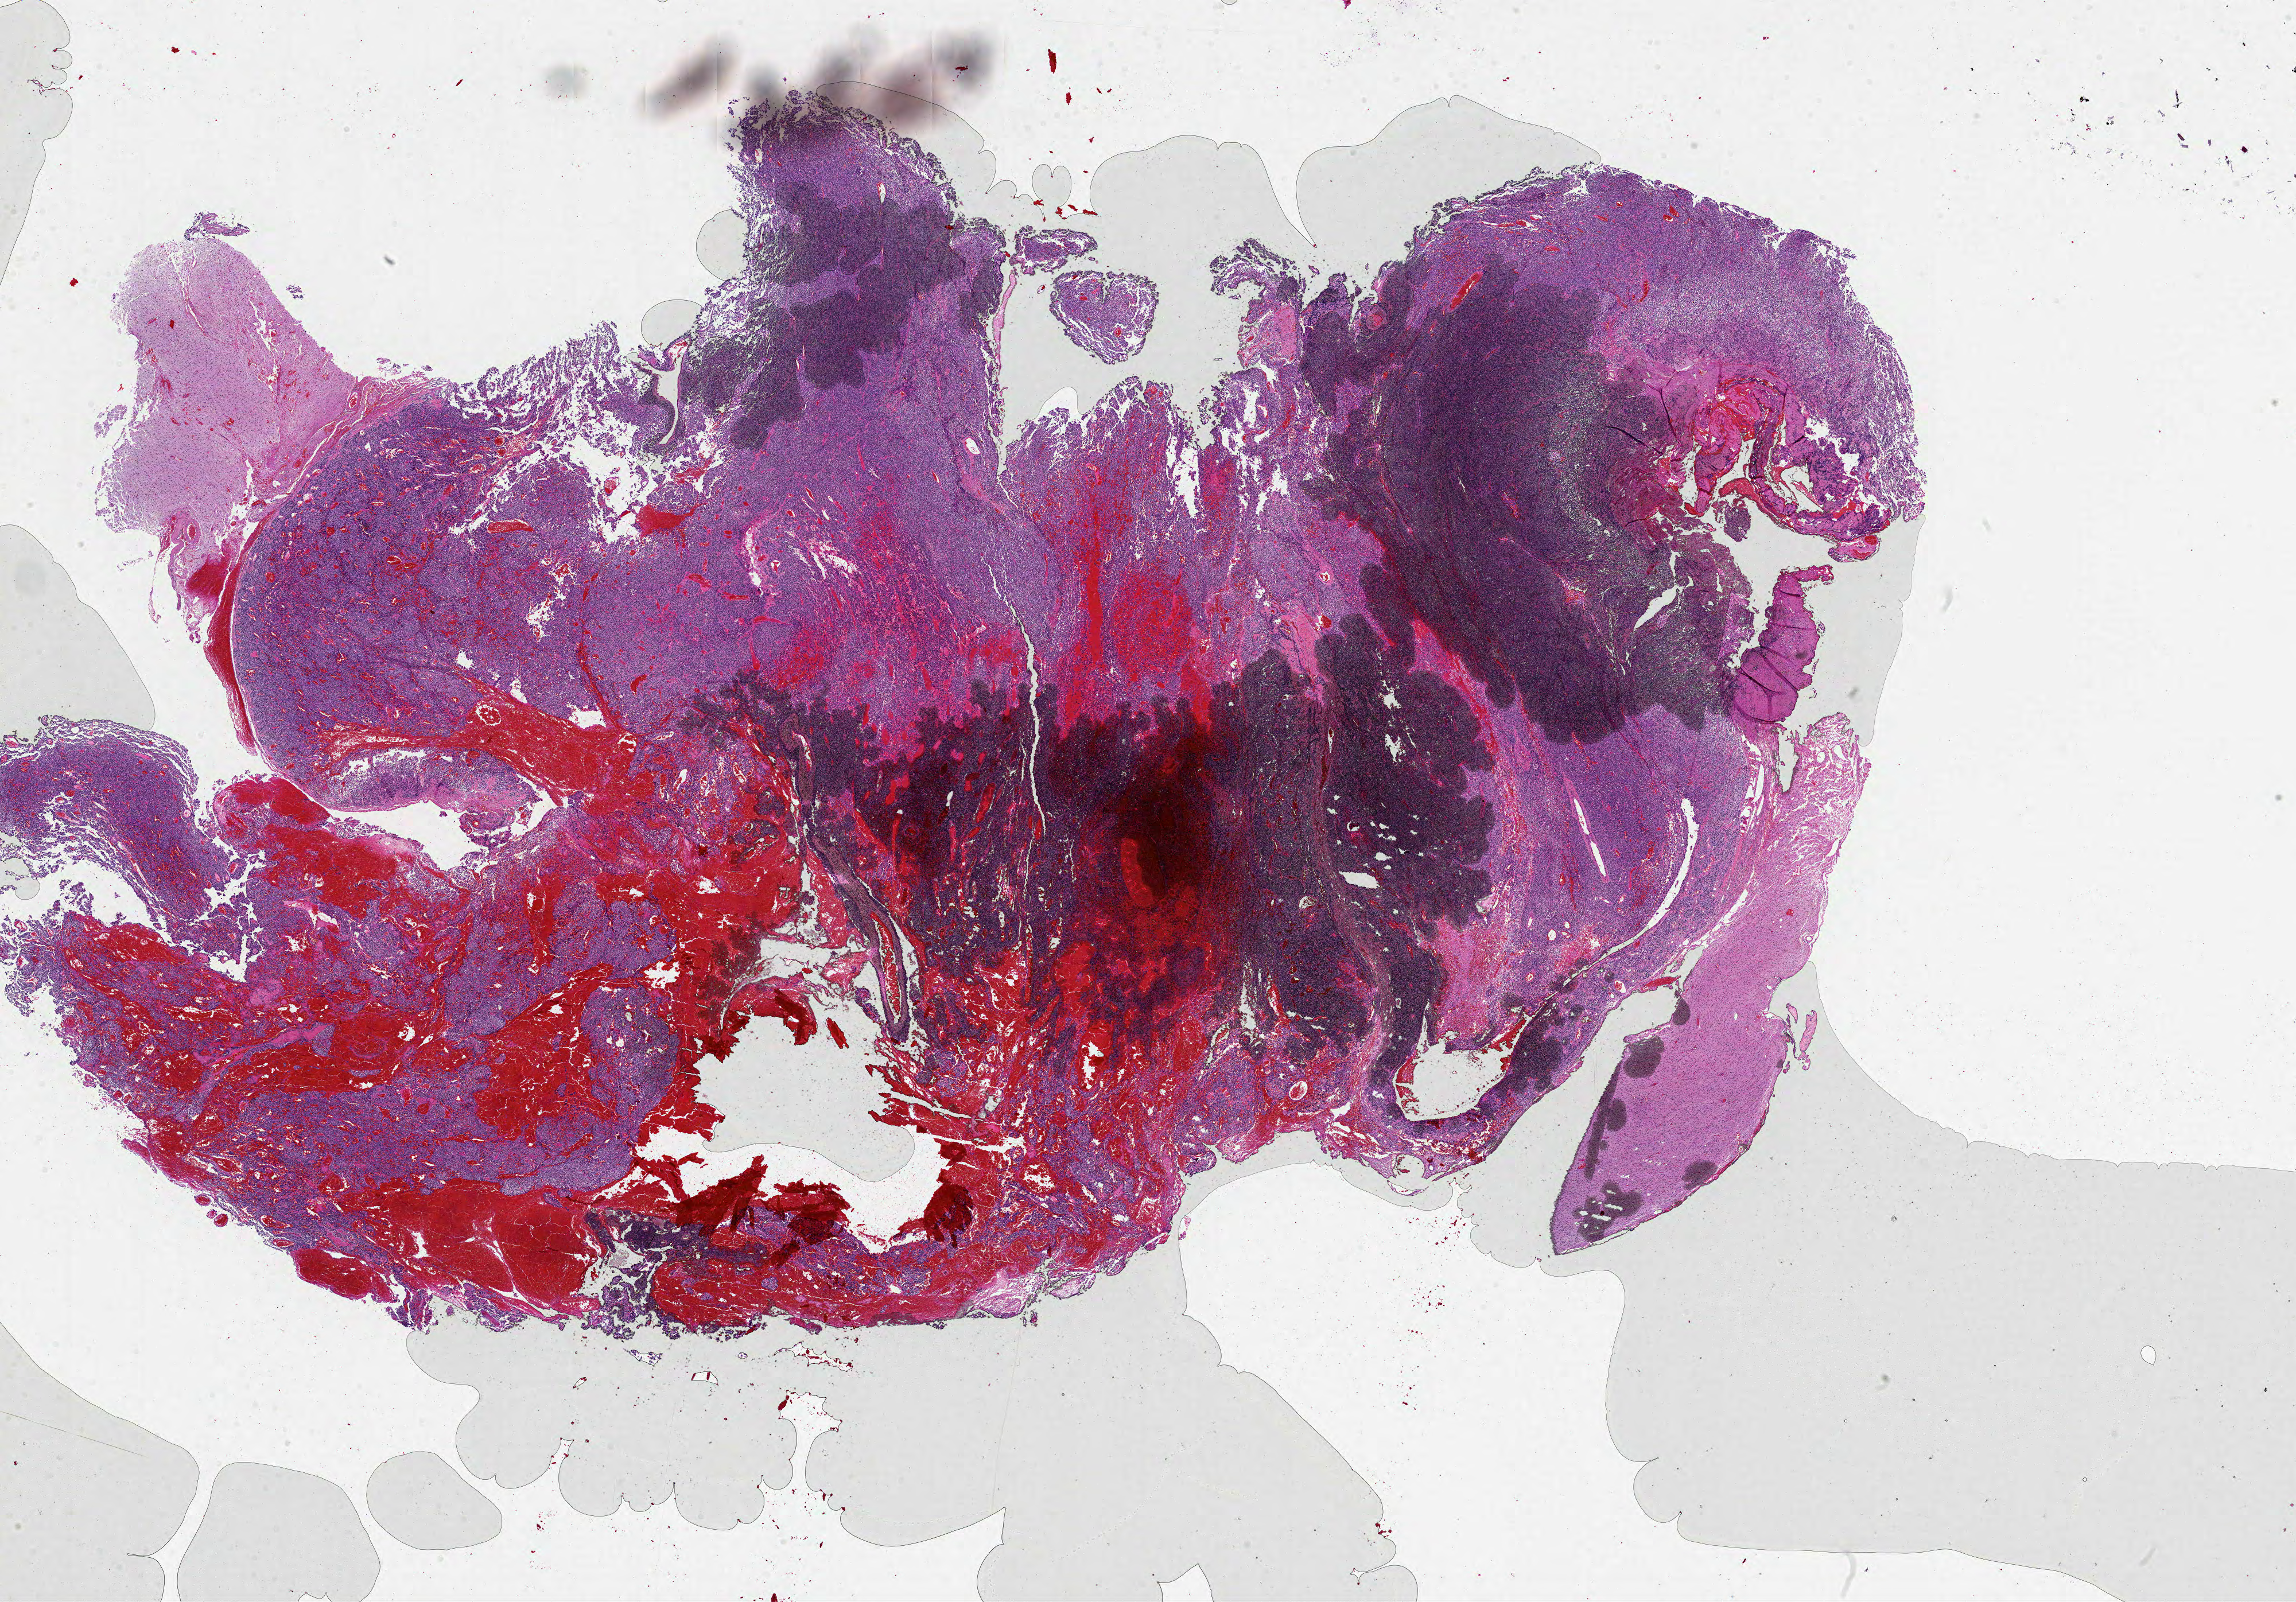
H&E-stained whole-slide image — whole scanned area (about 32.0 x 22.3 mm, acquisition: 20x scan) shown as a low-resolution overview, FFPE section, brain, primary tumour sample. Male, age 52 years at initial diagnosis.
Histologic diagnosis: Glioblastoma.